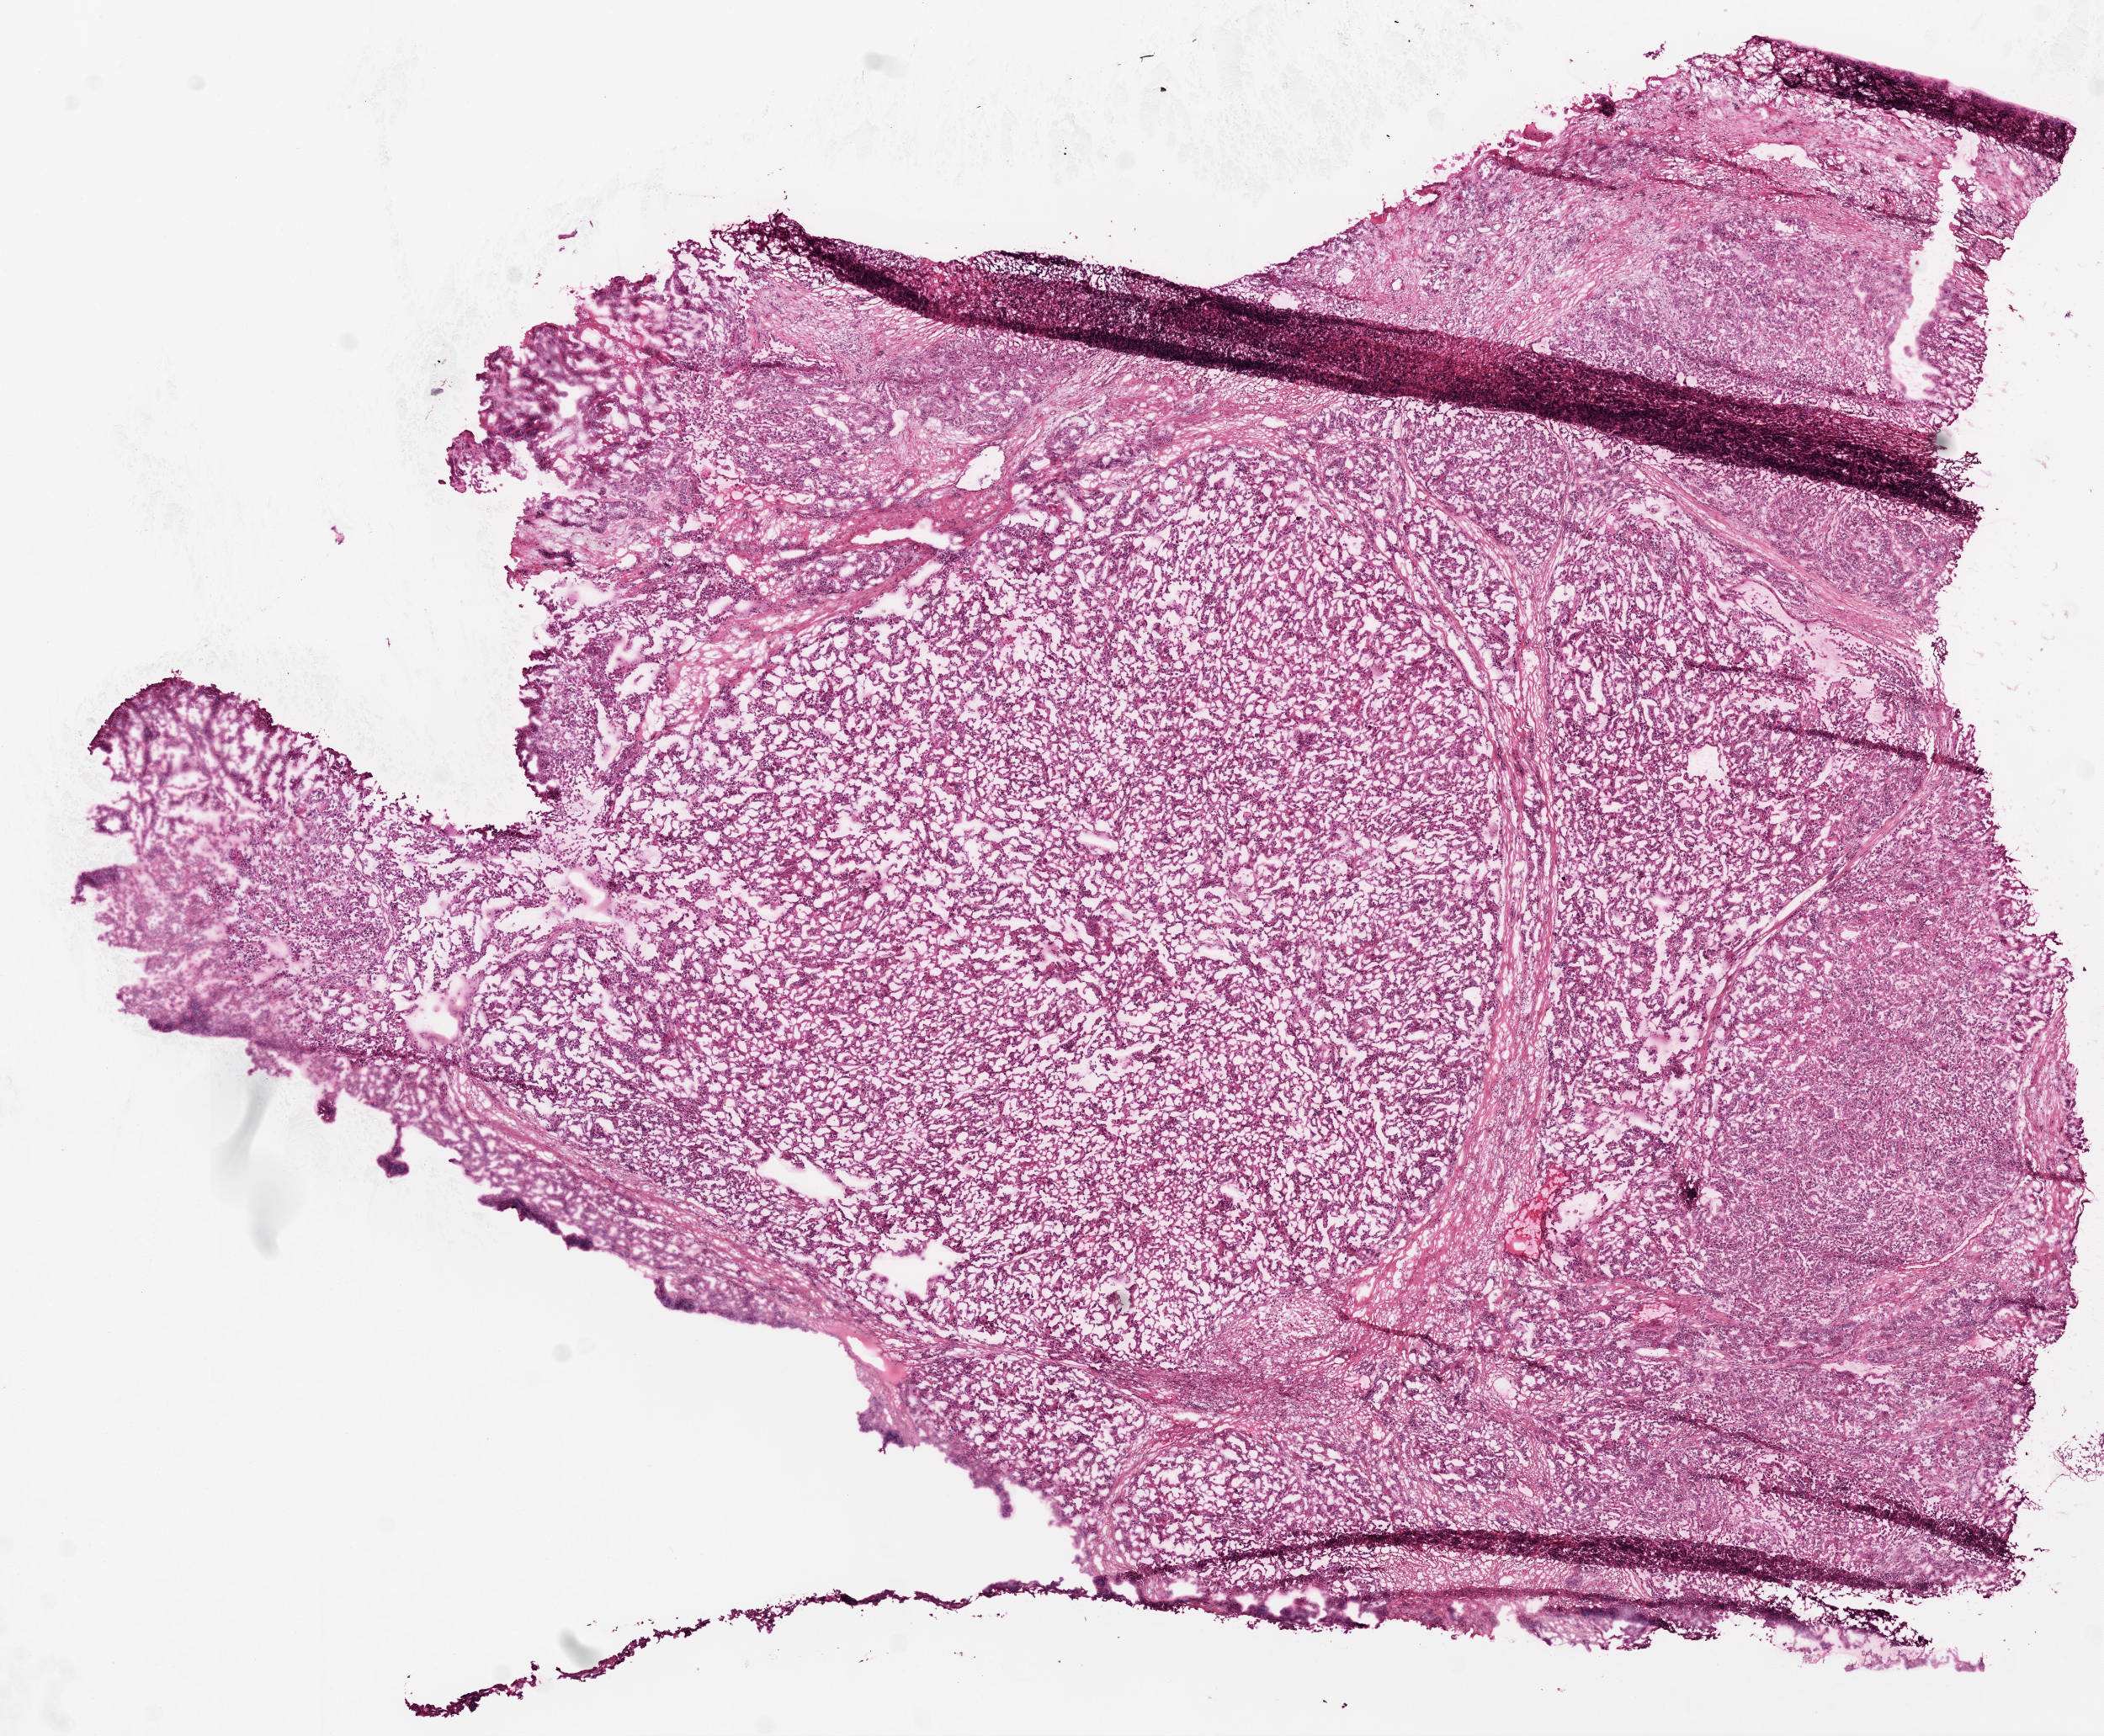
H&E-stained whole-slide image — a low-resolution overview of the entire scanned area, about 10.0 x 8.3 mm (from a 20x scan). Frozen section from the top of the tissue portion. Kidney, primary tumour sample. Male, age 41 years at initial diagnosis. Composition of this section per pathologist review: tumour cells 89%, tumour nuclei 80%, normal cells 0%, stromal cells 10%, necrosis 1%.
AJCC pathologic stage: IV (6th edition). Laterality: right. Pathologic diagnosis: Papillary adenocarcinoma, NOS.